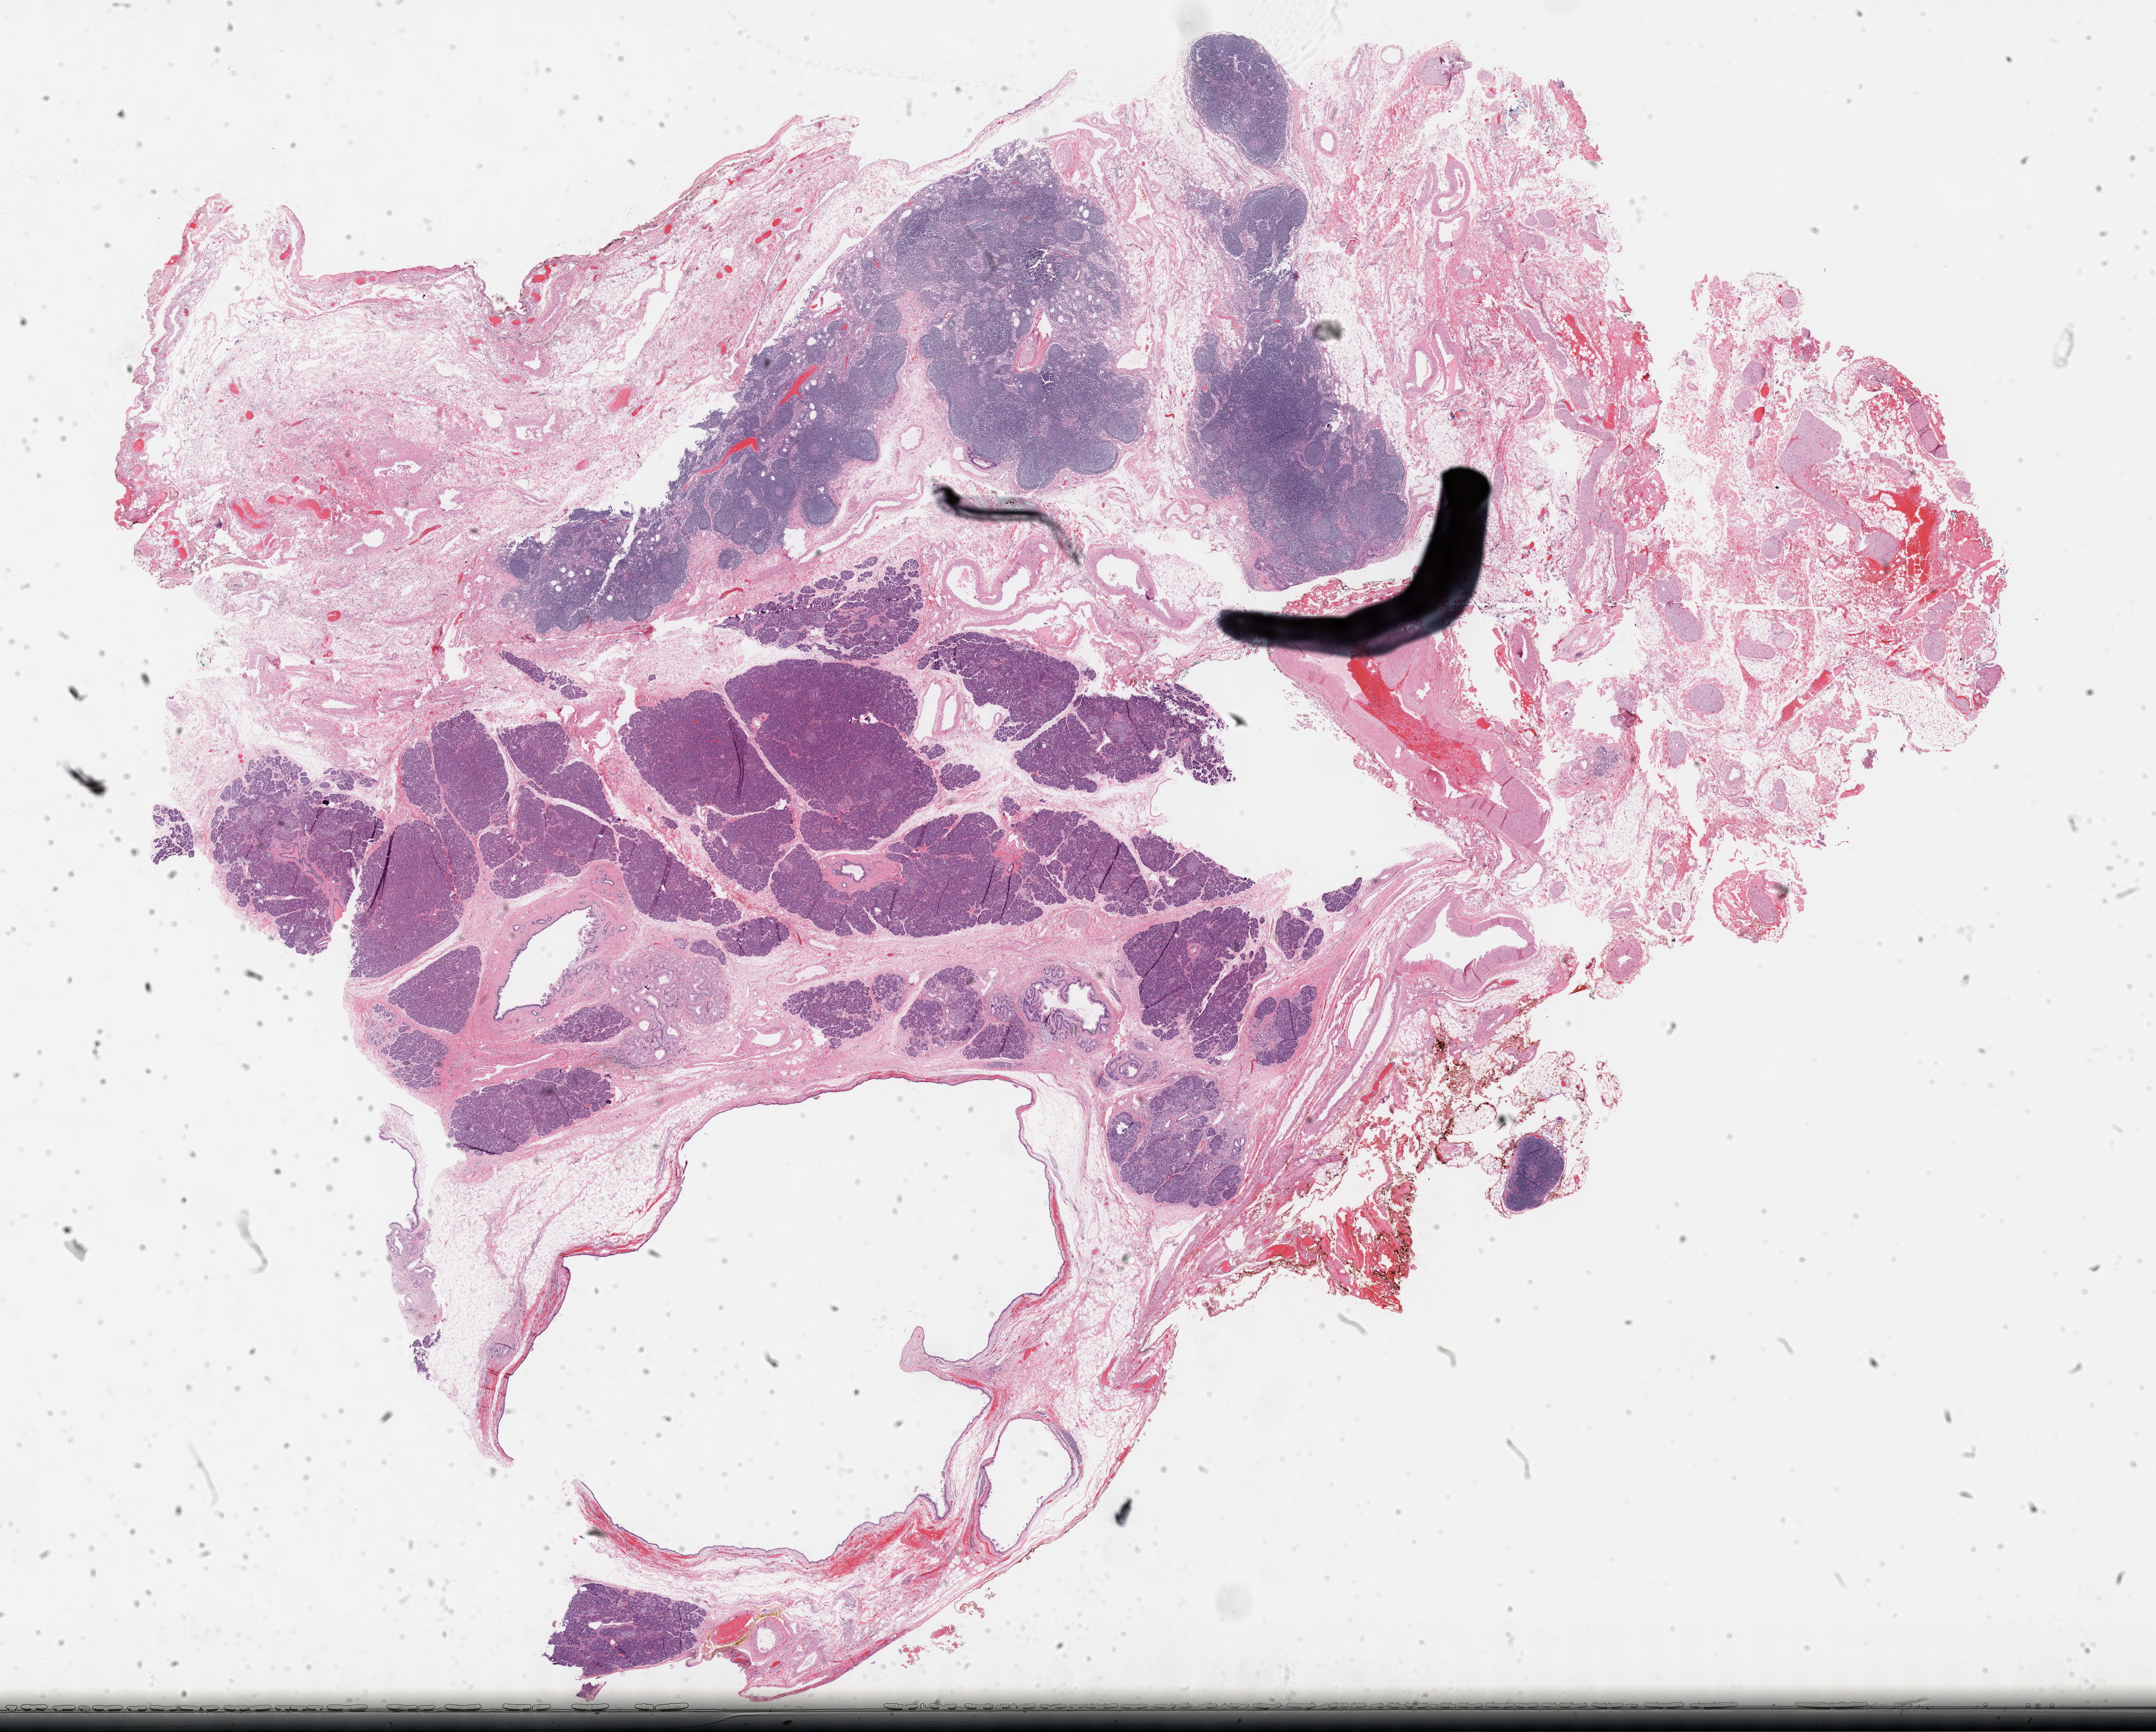
H&E whole-slide image — a low-resolution overview of the entire scanned area, about 29.2 x 23.5 mm; FFPE section; primary tumour sample from the pancreas. Female patient; age at initial diagnosis 57 years.
Histologic diagnosis: Infiltrating duct carcinoma, NOS (head of pancreas).